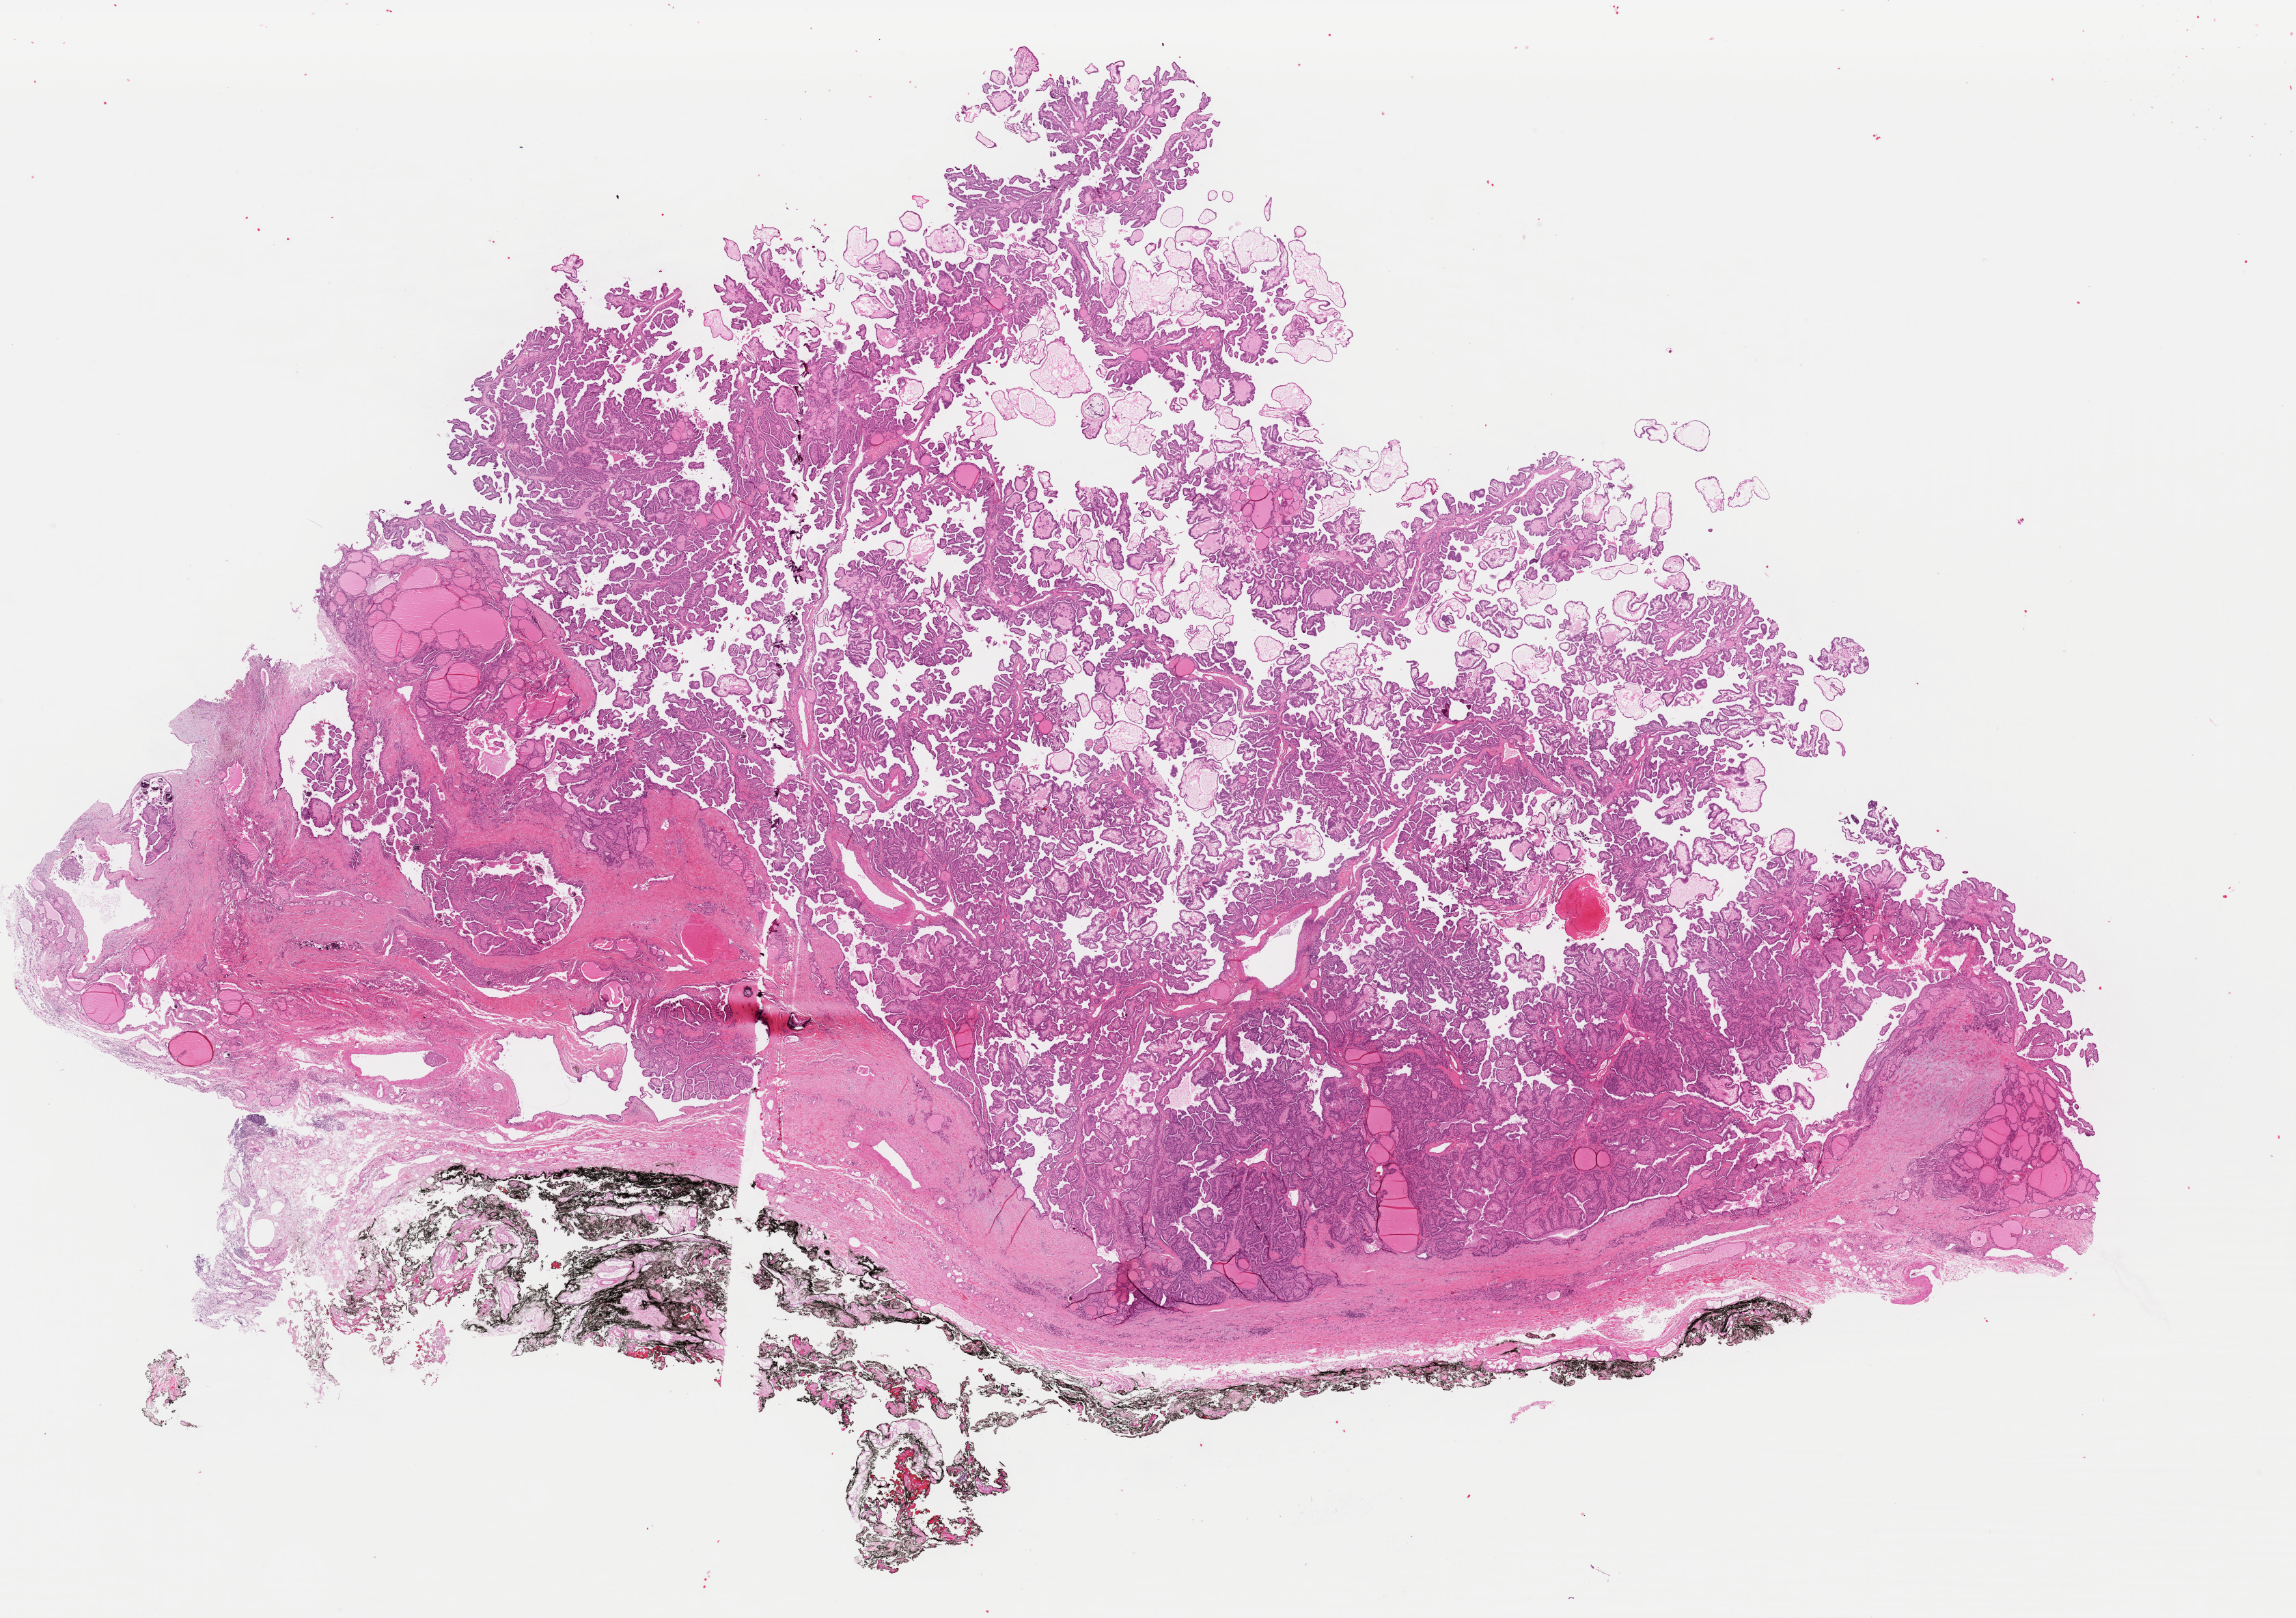
Digitized Hematoxylin and eosin (H&E) stained tissue section (whole slide) — low-resolution overview of the scanned area, about 26.5 x 18.7 mm (from a 40x scan). Formalin-fixed paraffin-embedded (FFPE) diagnostic section. Primary tumour sample from the thyroid. Male, age 39 years at initial diagnosis.
• lymph nodes positive (case pathology): 13 of 40 examined
• pathologic diagnosis: Papillary adenocarcinoma, NOS (thyroid gland)
• laterality: bilateral
• AJCC pathologic stage: I
• TNM: T3 N1b M0